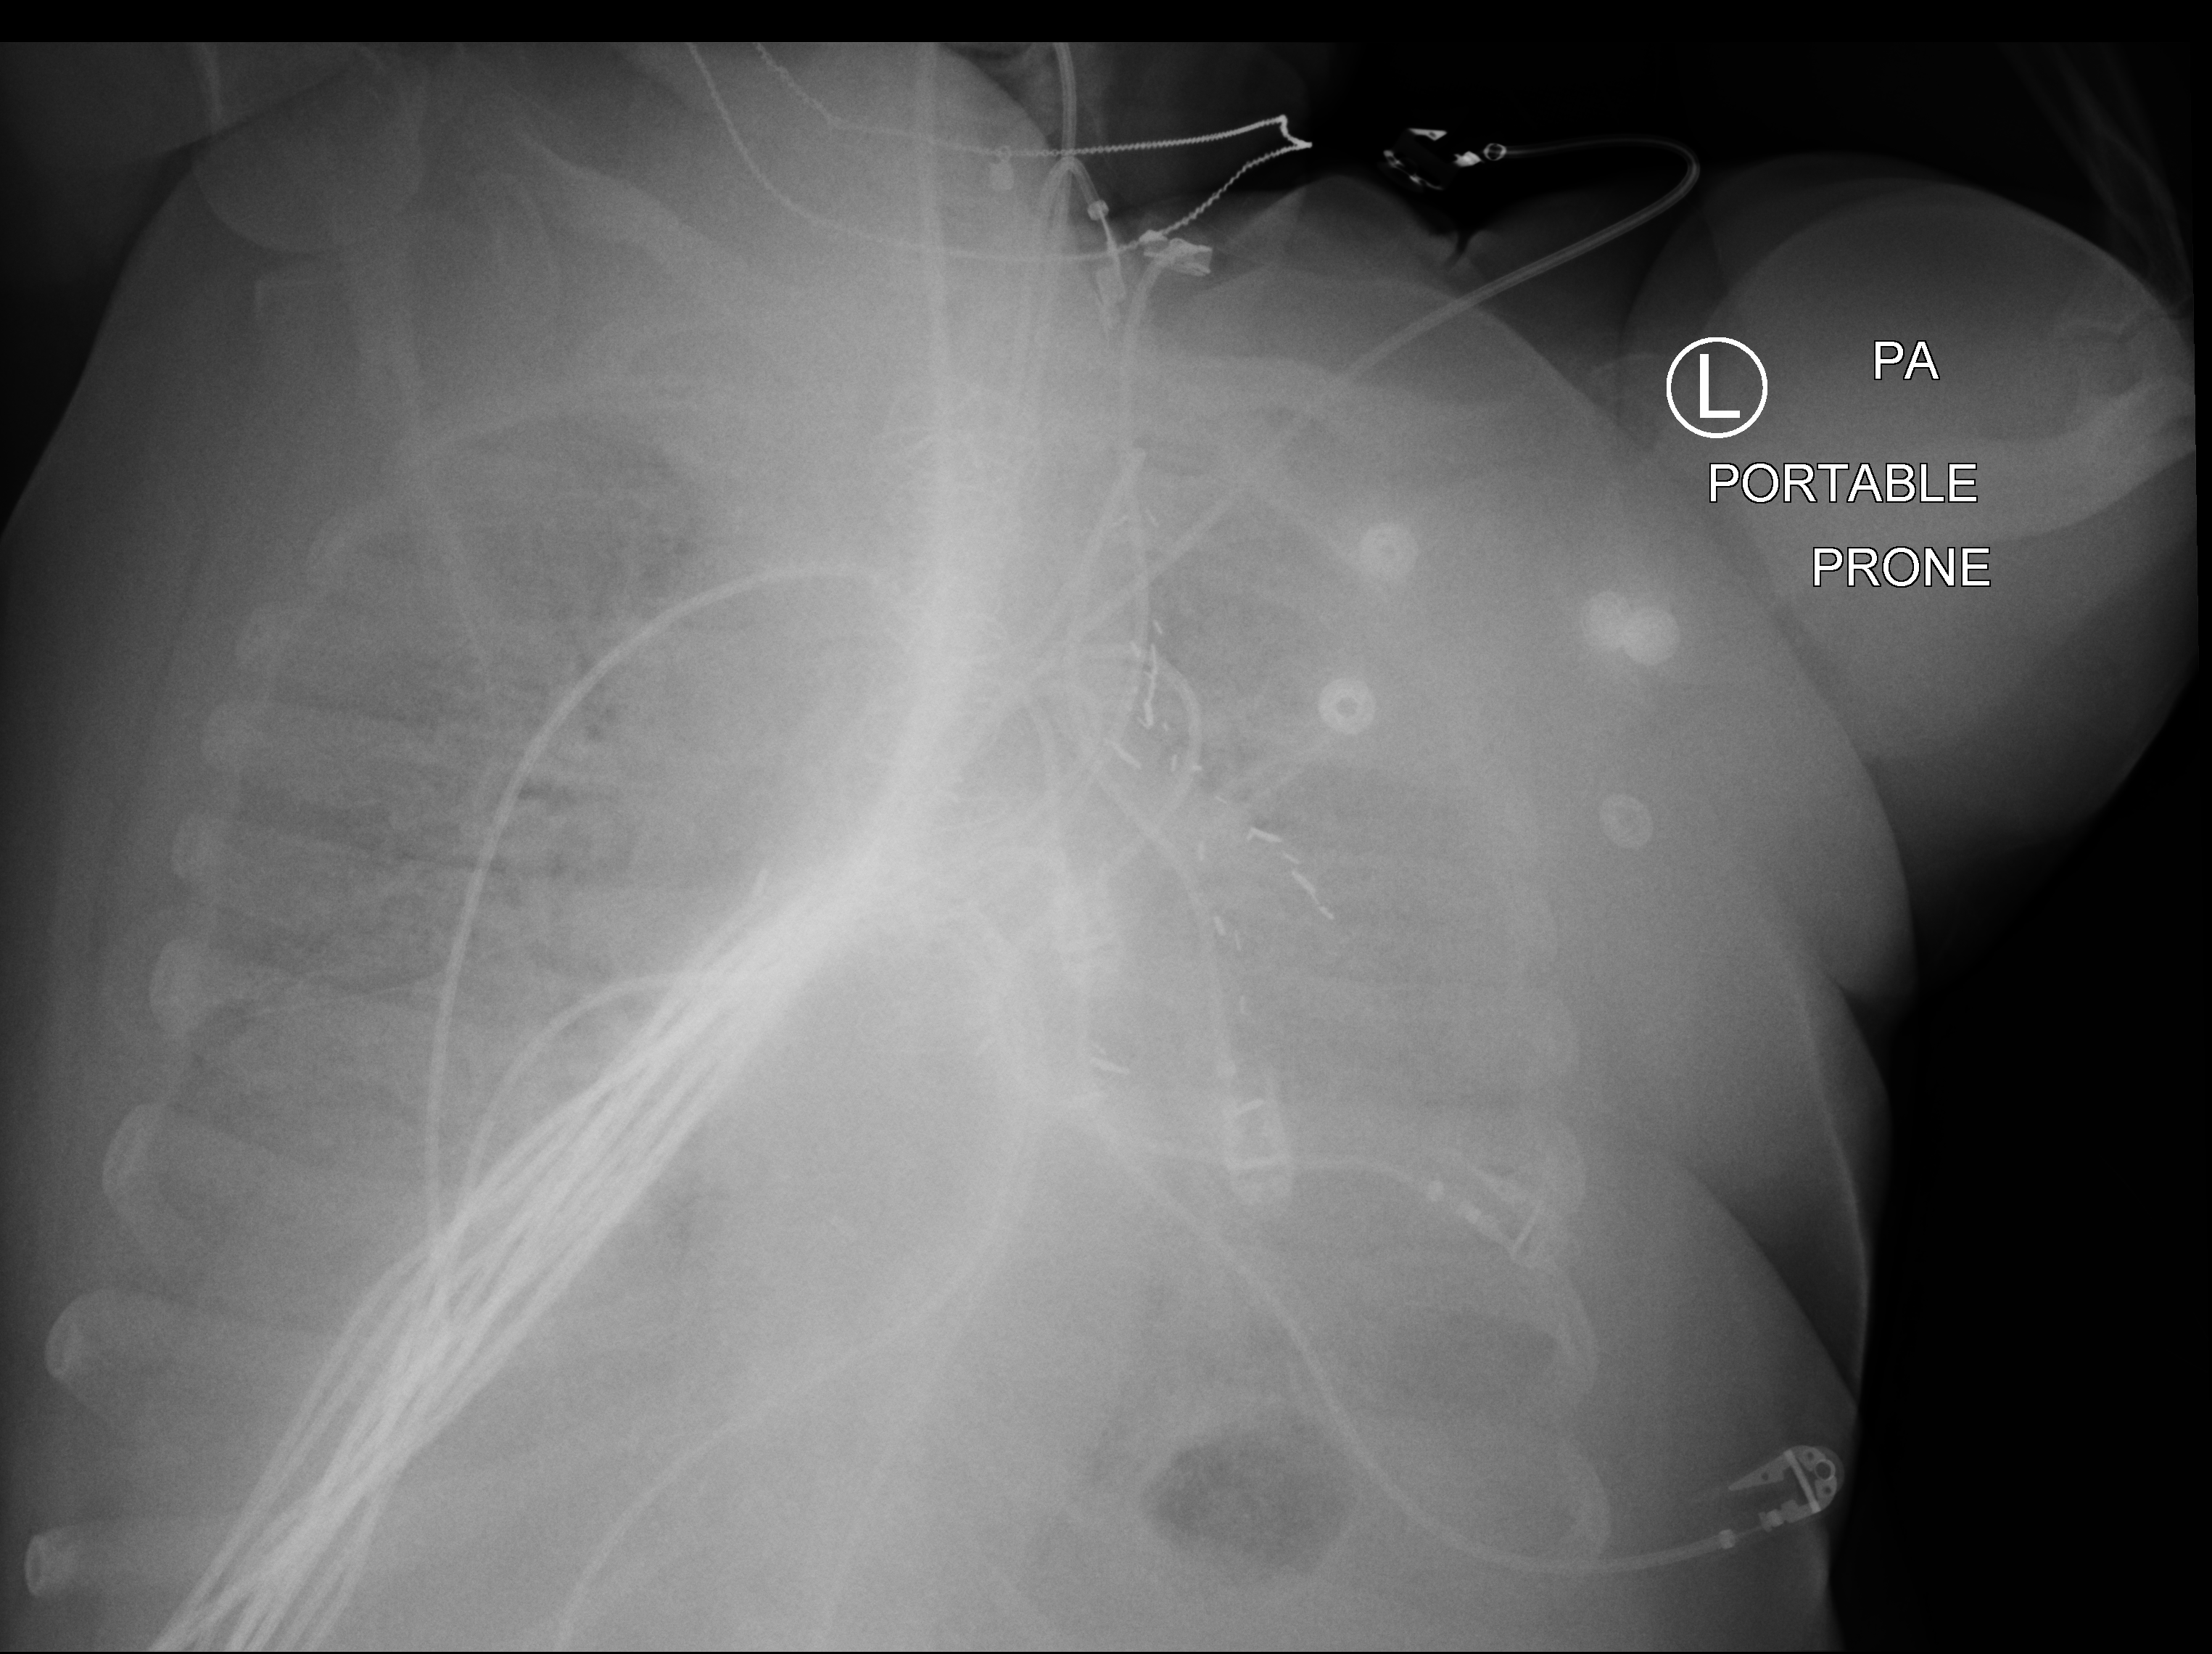
Bedside chest radiograph (computed radiography). Patient hospitalised with COVID-19; female, aged 60–74 years.
Admission-level facts for this patient (not findings on this image; timing relative to this image not recorded):
- chronic kidney disease (admission record): no
- hypertension (admission record): yes
- mechanically ventilated during this hospital stay: yes